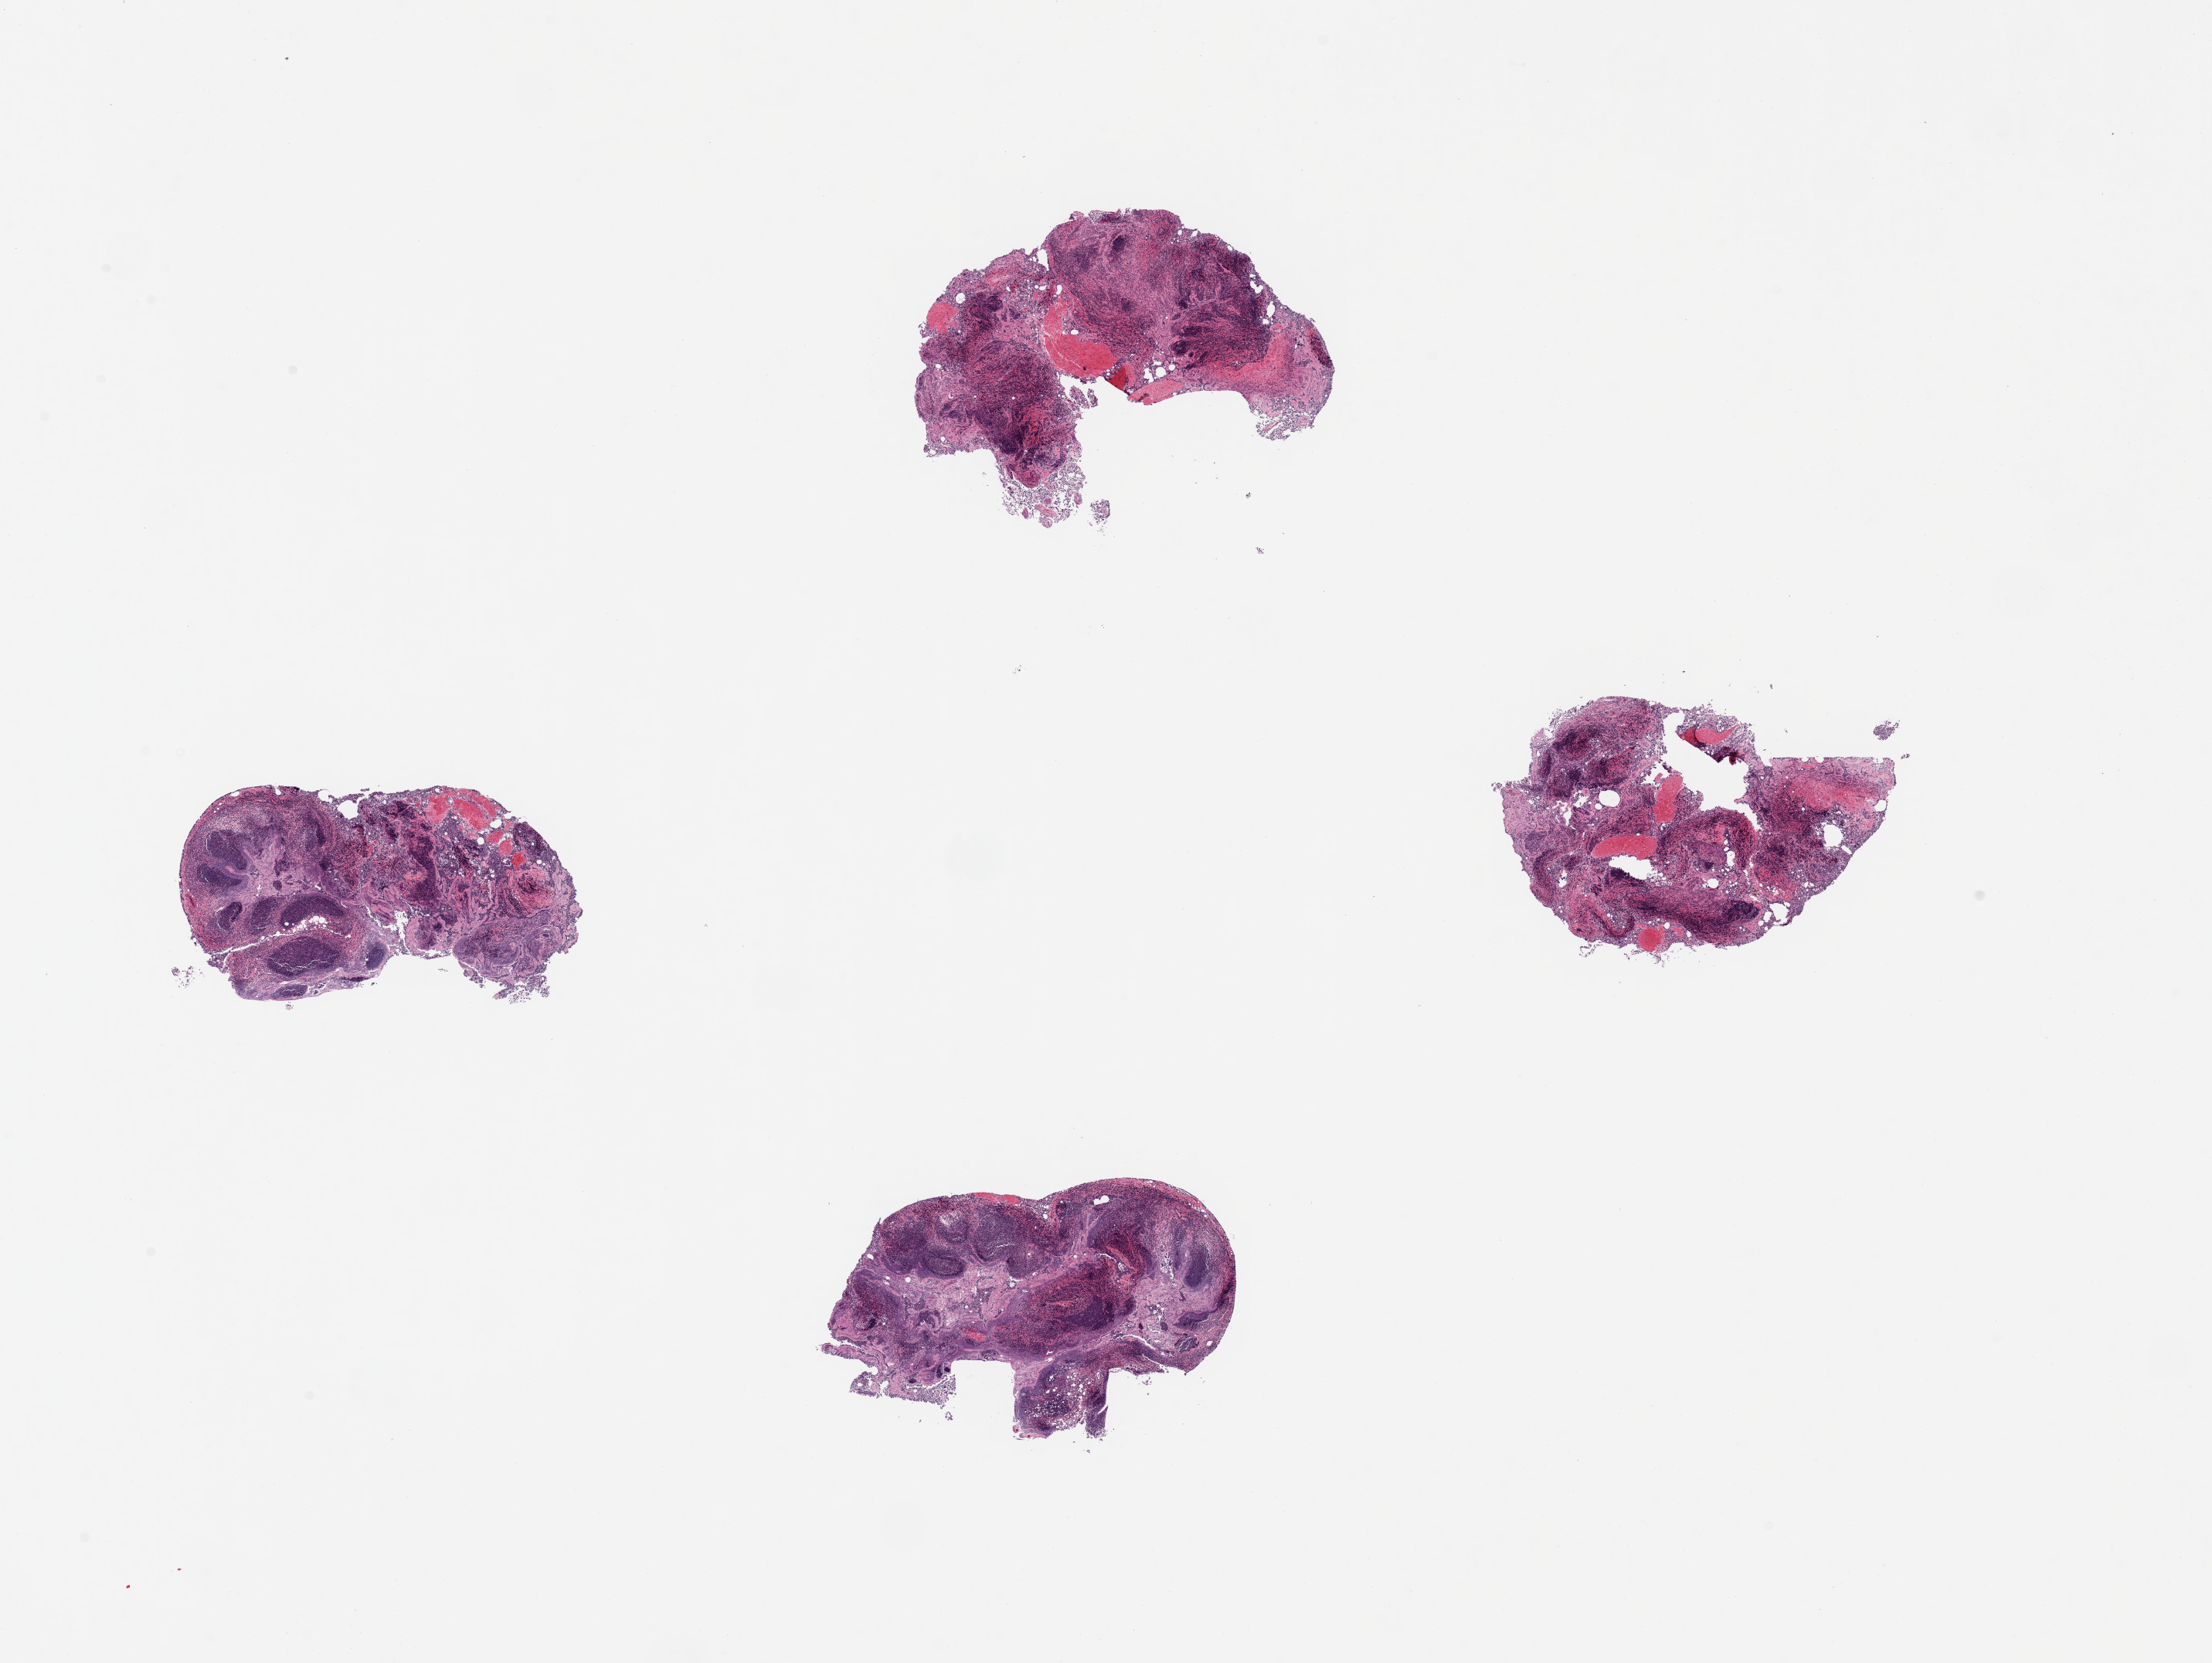
Digitized haematoxylin and eosin-stained section — a low-resolution overview of the entire scanned area, about 22.6 x 17.0 mm (slide scanned at 20x), PAXgene-fixed, paraffin-embedded tissue, target tissue: ileum, donor tissue sample. Donor sex: male.
• pathologist's review note for this sample: 4 pieces; lymphoid-rich specimens